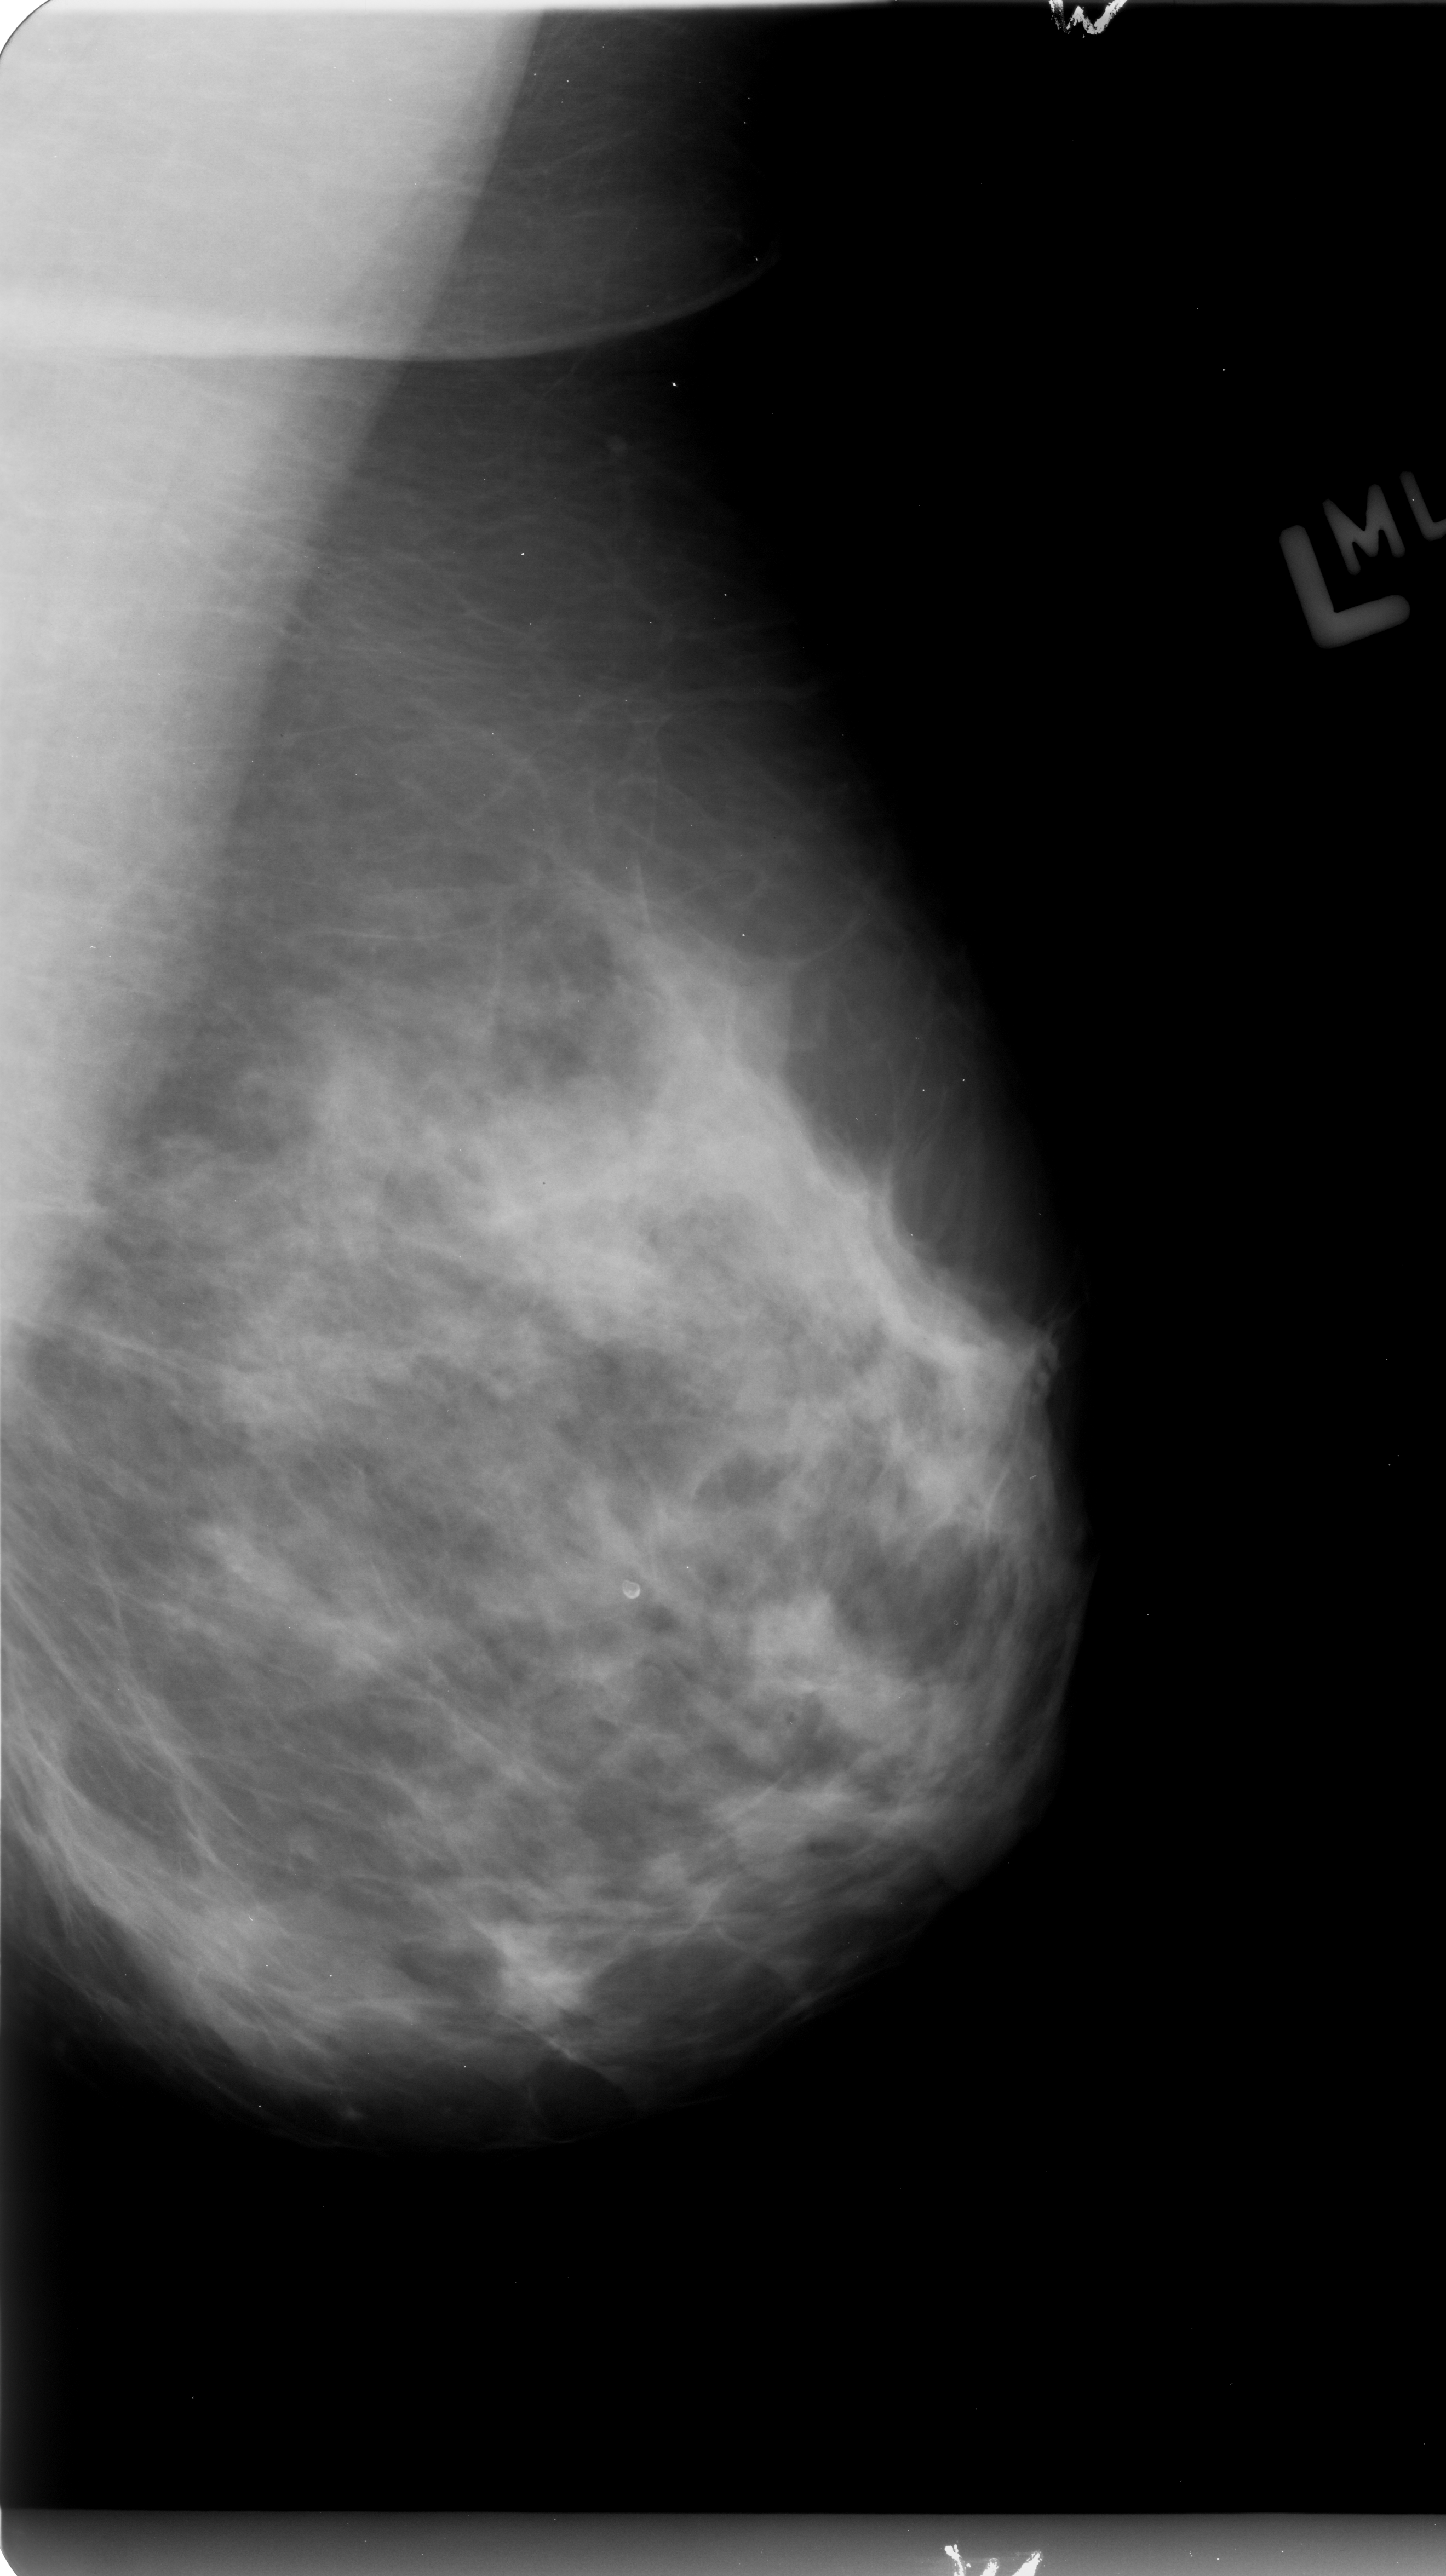
Scanned film-screen mammogram, left breast, MLO view, breast composition: heterogeneously dense (BI-RADS density category 3 of 4).
Calcifications, morphology punctate / pleomorphic, distribution clustered; BI-RADS assessment category 4; pathology result (as recorded, not read from the image): benign.